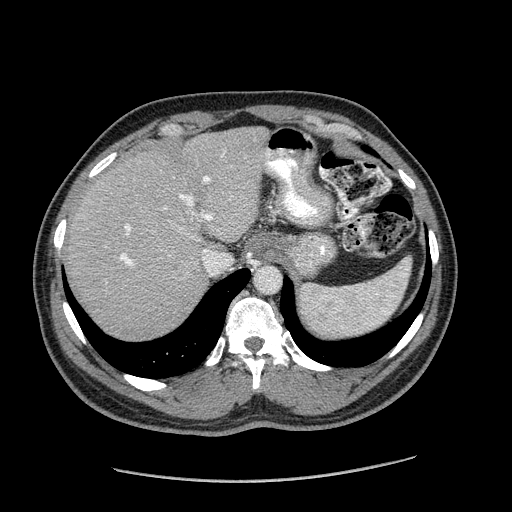
Contrast-enhanced abdominal CT (liver protocol), one axial slice. Slice 139 of 182 in the series (ordered by position). 120 kVp. Soft-tissue window (W 400 / L 40 HU). 2.5 mm slice thickness. 512 × 512 image matrix, field of view 400 × 400 mm. From the clinical record (not read from this slice): diagnosis: hepatocellular carcinoma (patient treated with transarterial chemoembolisation; whether this scan precedes or follows treatment is not stated here); TNM stage (as recorded): Stage-I; Child-Pugh class: A.
Outlined on this slice (semi-automatic segmentation, software-assisted and operator-edited):
- liver parenchyma outside the tumour (the mass and vessels are separate outlines, so this box may not span the whole liver): box from (x=65, y=126) to (x=268, y=338) px
- liver vessels: (x=120, y=154)–(x=224, y=266)